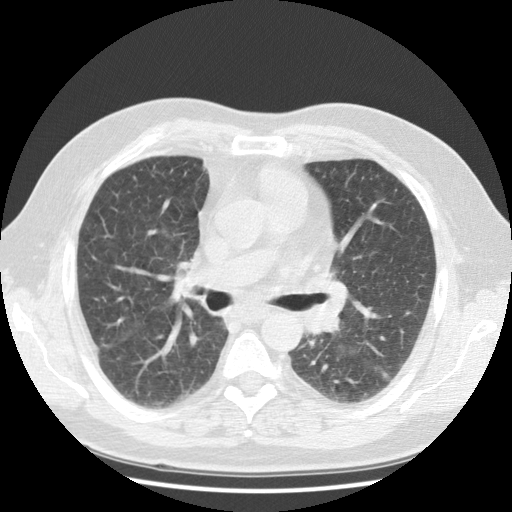
Low-dose screening chest CT, one axial slice; slice 66 of 108 in the series (ordered by position); reconstruction kernel STANDARD; 120 kVp; lung window (W 1500 / L -600 HU); 2.5 mm slice thickness; 512 × 512 image matrix.
Outlined on this slice (manually delineated by an expert):
- lesion 1 (tumor, hilum of left lung): box from (x=304, y=297) to (x=344, y=335) px